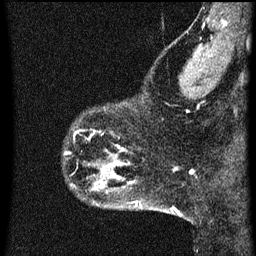
Breast MRI (dynamic contrast-enhanced), one sagittal slice. Slice 11 of 60 in the series (ordered by position). Dynamic contrast-enhanced series, image 2 of 3 at this slice position (ordered by acquisition). 1.5 T. TE 4.2 ms, TR 8 ms. 256 × 256 image matrix. Patient: female, 43 years.
Outlined on this slice (semi-automatically segmented with operator editing):
- analysis volume of interest (the breast-tissue region the enhancement analysis was run in; not a lesion): box from (x=64, y=106) to (x=104, y=153) px
- tumour enhancement mask (voxels above the 70 % enhancement threshold inside the analysis volume of interest): (x=73, y=130)–(x=92, y=141)